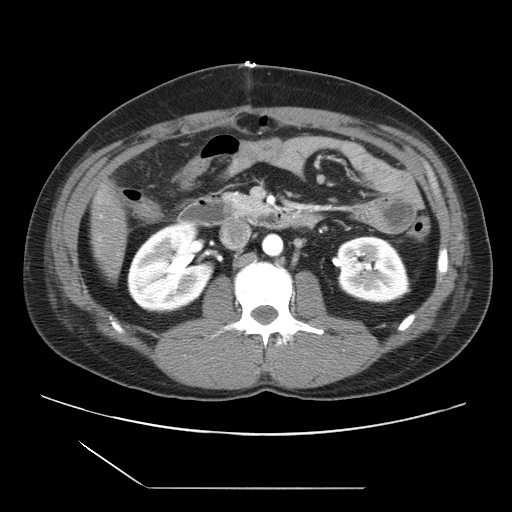
Contrast-enhanced abdominal CT, one axial slice; slice 4 of 39 in the series (ordered by position); 120 kVp; intravenous contrast given; soft-tissue window (W 400 / L 40 HU); 512 × 512 image matrix, field of view 395 × 395 mm. Male patient, age 39 years. From the clinical record (not read from this slice): diagnosis: colorectal cancer liver metastases, imaged before liver resection; multiple liver metastases: yes; largest metastasis: 1.3 cm; disease in both lobes: no.
Outlined on this slice (manually delineated by an expert):
- liver: box from (x=92, y=189) to (x=128, y=279) px